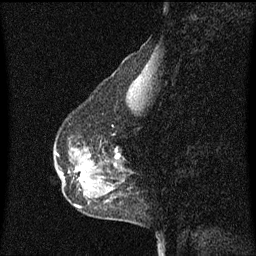
Breast MRI (dynamic contrast-enhanced), one sagittal slice; slice 20 of 60 in the series (ordered by position); dynamic contrast-enhanced series, image 2 of 3 at this slice position (ordered by acquisition); 1.5 T; TE 4.2 ms, TR 8.4 ms; 2 mm slice thickness; 256 × 256 image matrix. Female patient, age 50 years. Case-level facts recorded for this patient, not image findings: setting: breast cancer imaged before/during neoadjuvant chemotherapy; receptor status: HR-positive, HER2-negative.
Outlined on this slice (semi-automatically segmented with operator editing):
- analysis volume of interest (the breast-tissue region the enhancement analysis was run in; not a lesion): box from (x=61, y=144) to (x=126, y=189) px
- tumour enhancement mask (voxels above the 70 % enhancement threshold inside the analysis volume of interest): (x=82, y=164)–(x=117, y=177)